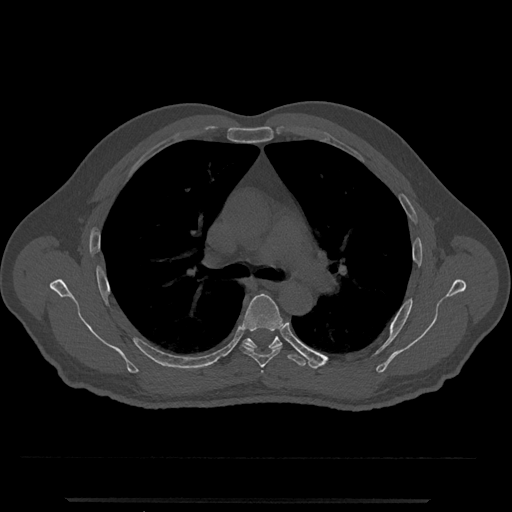
CT including the spine, one axial slice. Position 773 of 797 along the scan axis. Reconstruction kernel Br40s/3. 120 kVp. Bone window (W 1800 / L 400 HU). 0.5 mm slice thickness. 512 × 512 image matrix, field of view 419 × 419 mm. Male patient, age 63 years. From the clinical record (not read from this slice): primary cancer: prostate.
Annotated regions visible in this slice (semi-automatic segmentation, software-assisted and operator-edited):
- T5 vertebra: bounding box [x1, y1, x2, y2] px = [239, 294, 283, 368]
- T6 vertebra: [243, 335, 306, 367]